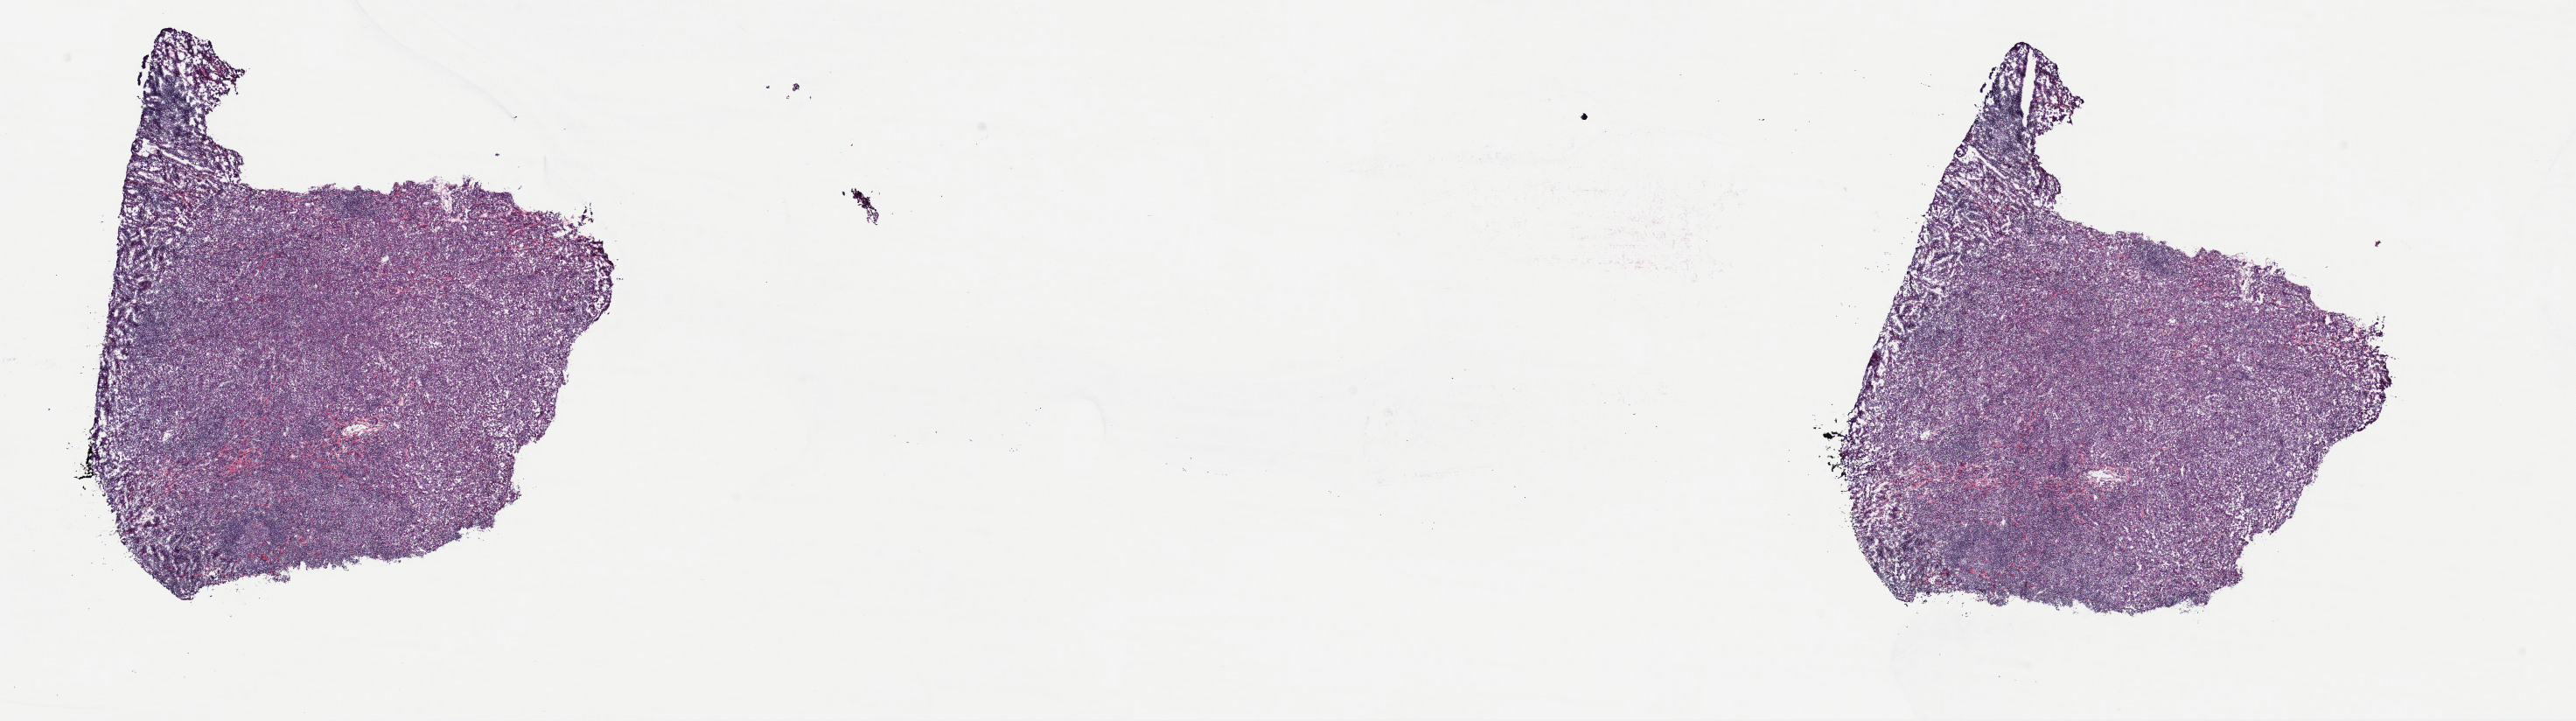
H&E whole-slide image, whole scanned area (about 23.3 x 6.5 mm, acquisition: 40x scan) shown as a low-resolution overview. Frozen section. Metastatic tumour sample, sampled site: lymph nodes of axilla or arm. Patient: female, age at initial diagnosis 48 years. Composition of this section per pathologist review: tumour cells 65%, tumour nuclei 65%, normal cells 0%, stromal cells 35%, necrosis 0%. Inflammatory infiltration, as recorded: lymphocyte infiltration 12%, monocyte infiltration 2%, neutrophil infiltration 3%.
This section: metastatic tumour tissue. Patient diagnosis: Malignant melanoma, NOS.